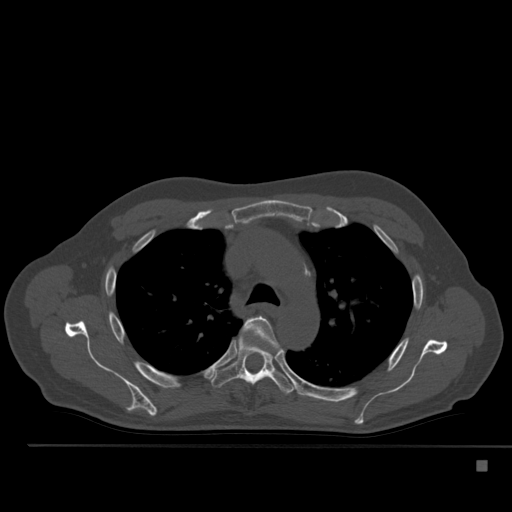
CT including the spine, one axial slice. Slice 371 of 517 in the series (ordered by position). Bone window (W 1800 / L 400 HU). 512 × 512 image matrix. Male patient, age 70 years. Case-level facts recorded for this patient, not image findings: primary cancer: renal; vertebrae with lytic lesions (as recorded): T4, T6, T10, T12, L3, L4, L5.
Outlined on this slice (semi-automatic segmentation, software-assisted and operator-edited):
- T4 vertebra: box from (x=245, y=316) to (x=279, y=351) px
- T5 vertebra: (x=211, y=334)–(x=296, y=394)